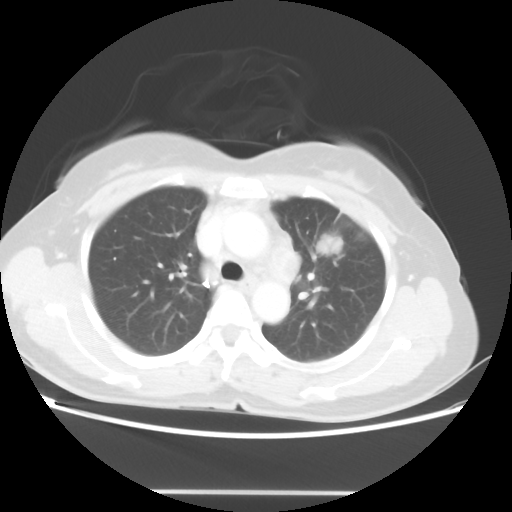
Chest CT, one axial slice. Slice 33 of 46 in the series (ordered by position). 100 kVp. Lung window (W 1500 / L -600 HU). 5 mm slice thickness. 512 × 512 image matrix. Female patient, age 50 years. From the clinical record (not read from this slice): clinical TNM (as recorded): T1c N1 M0; histopathological grade: G3.
Outlined on this slice (bounding box drawn by a radiologist):
- lung tumour (recorded histology: adenocarcinoma): bounding box [x1, y1, x2, y2] px = [319, 235, 344, 253]